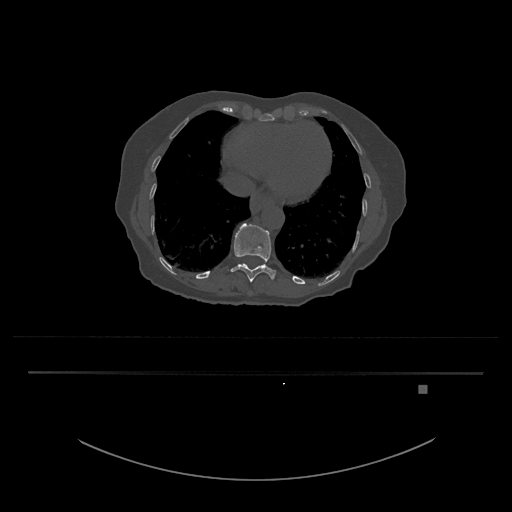
CT including the spine, one axial slice. Slice 663 of 797 in the series (ordered by position). Bone window (W 1800 / L 400 HU). 512 × 512 image matrix, field of view 500 × 500 mm. Female patient, age 57 years. Case-level facts recorded for this patient, not image findings: primary cancer: cervical.
Annotated regions visible in this slice (semi-automatic segmentation, software-assisted and operator-edited):
- T11 vertebra: bounding box <231,223,276,283> (left, top, right, bottom; pixels)
- T12 vertebra: <239,263,247,265>